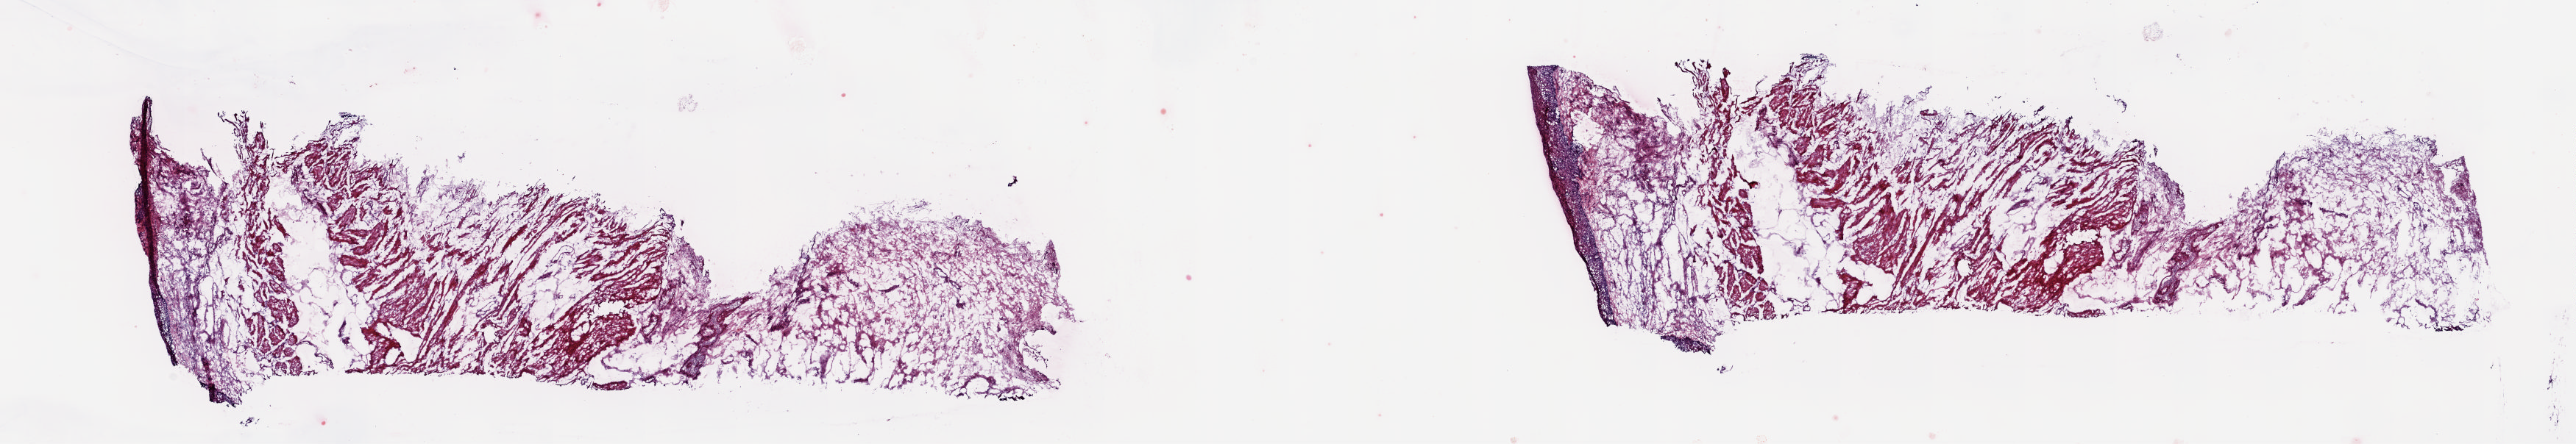
H&E-stained whole-slide image, low-resolution overview of the scanned area, about 27.8 x 4.8 mm (acquisition: 20x scan); frozen section from the top of the tissue portion; stomach, solid tissue normal (non-tumour tissue) sample. Patient: female, age at initial diagnosis 78 years. Slide review estimates, as recorded: tumour cells 0%, tumour nuclei 0%, normal cells 100%, stromal cells 0%, necrosis 0%. Infiltration values recorded for this section: lymphocyte infiltration 2%, monocyte infiltration 0%, neutrophil infiltration 0%.
This section: solid tissue normal sample (biorepository sample class). Patient diagnosis: Adenocarcinoma, NOS (cardia, NOS).